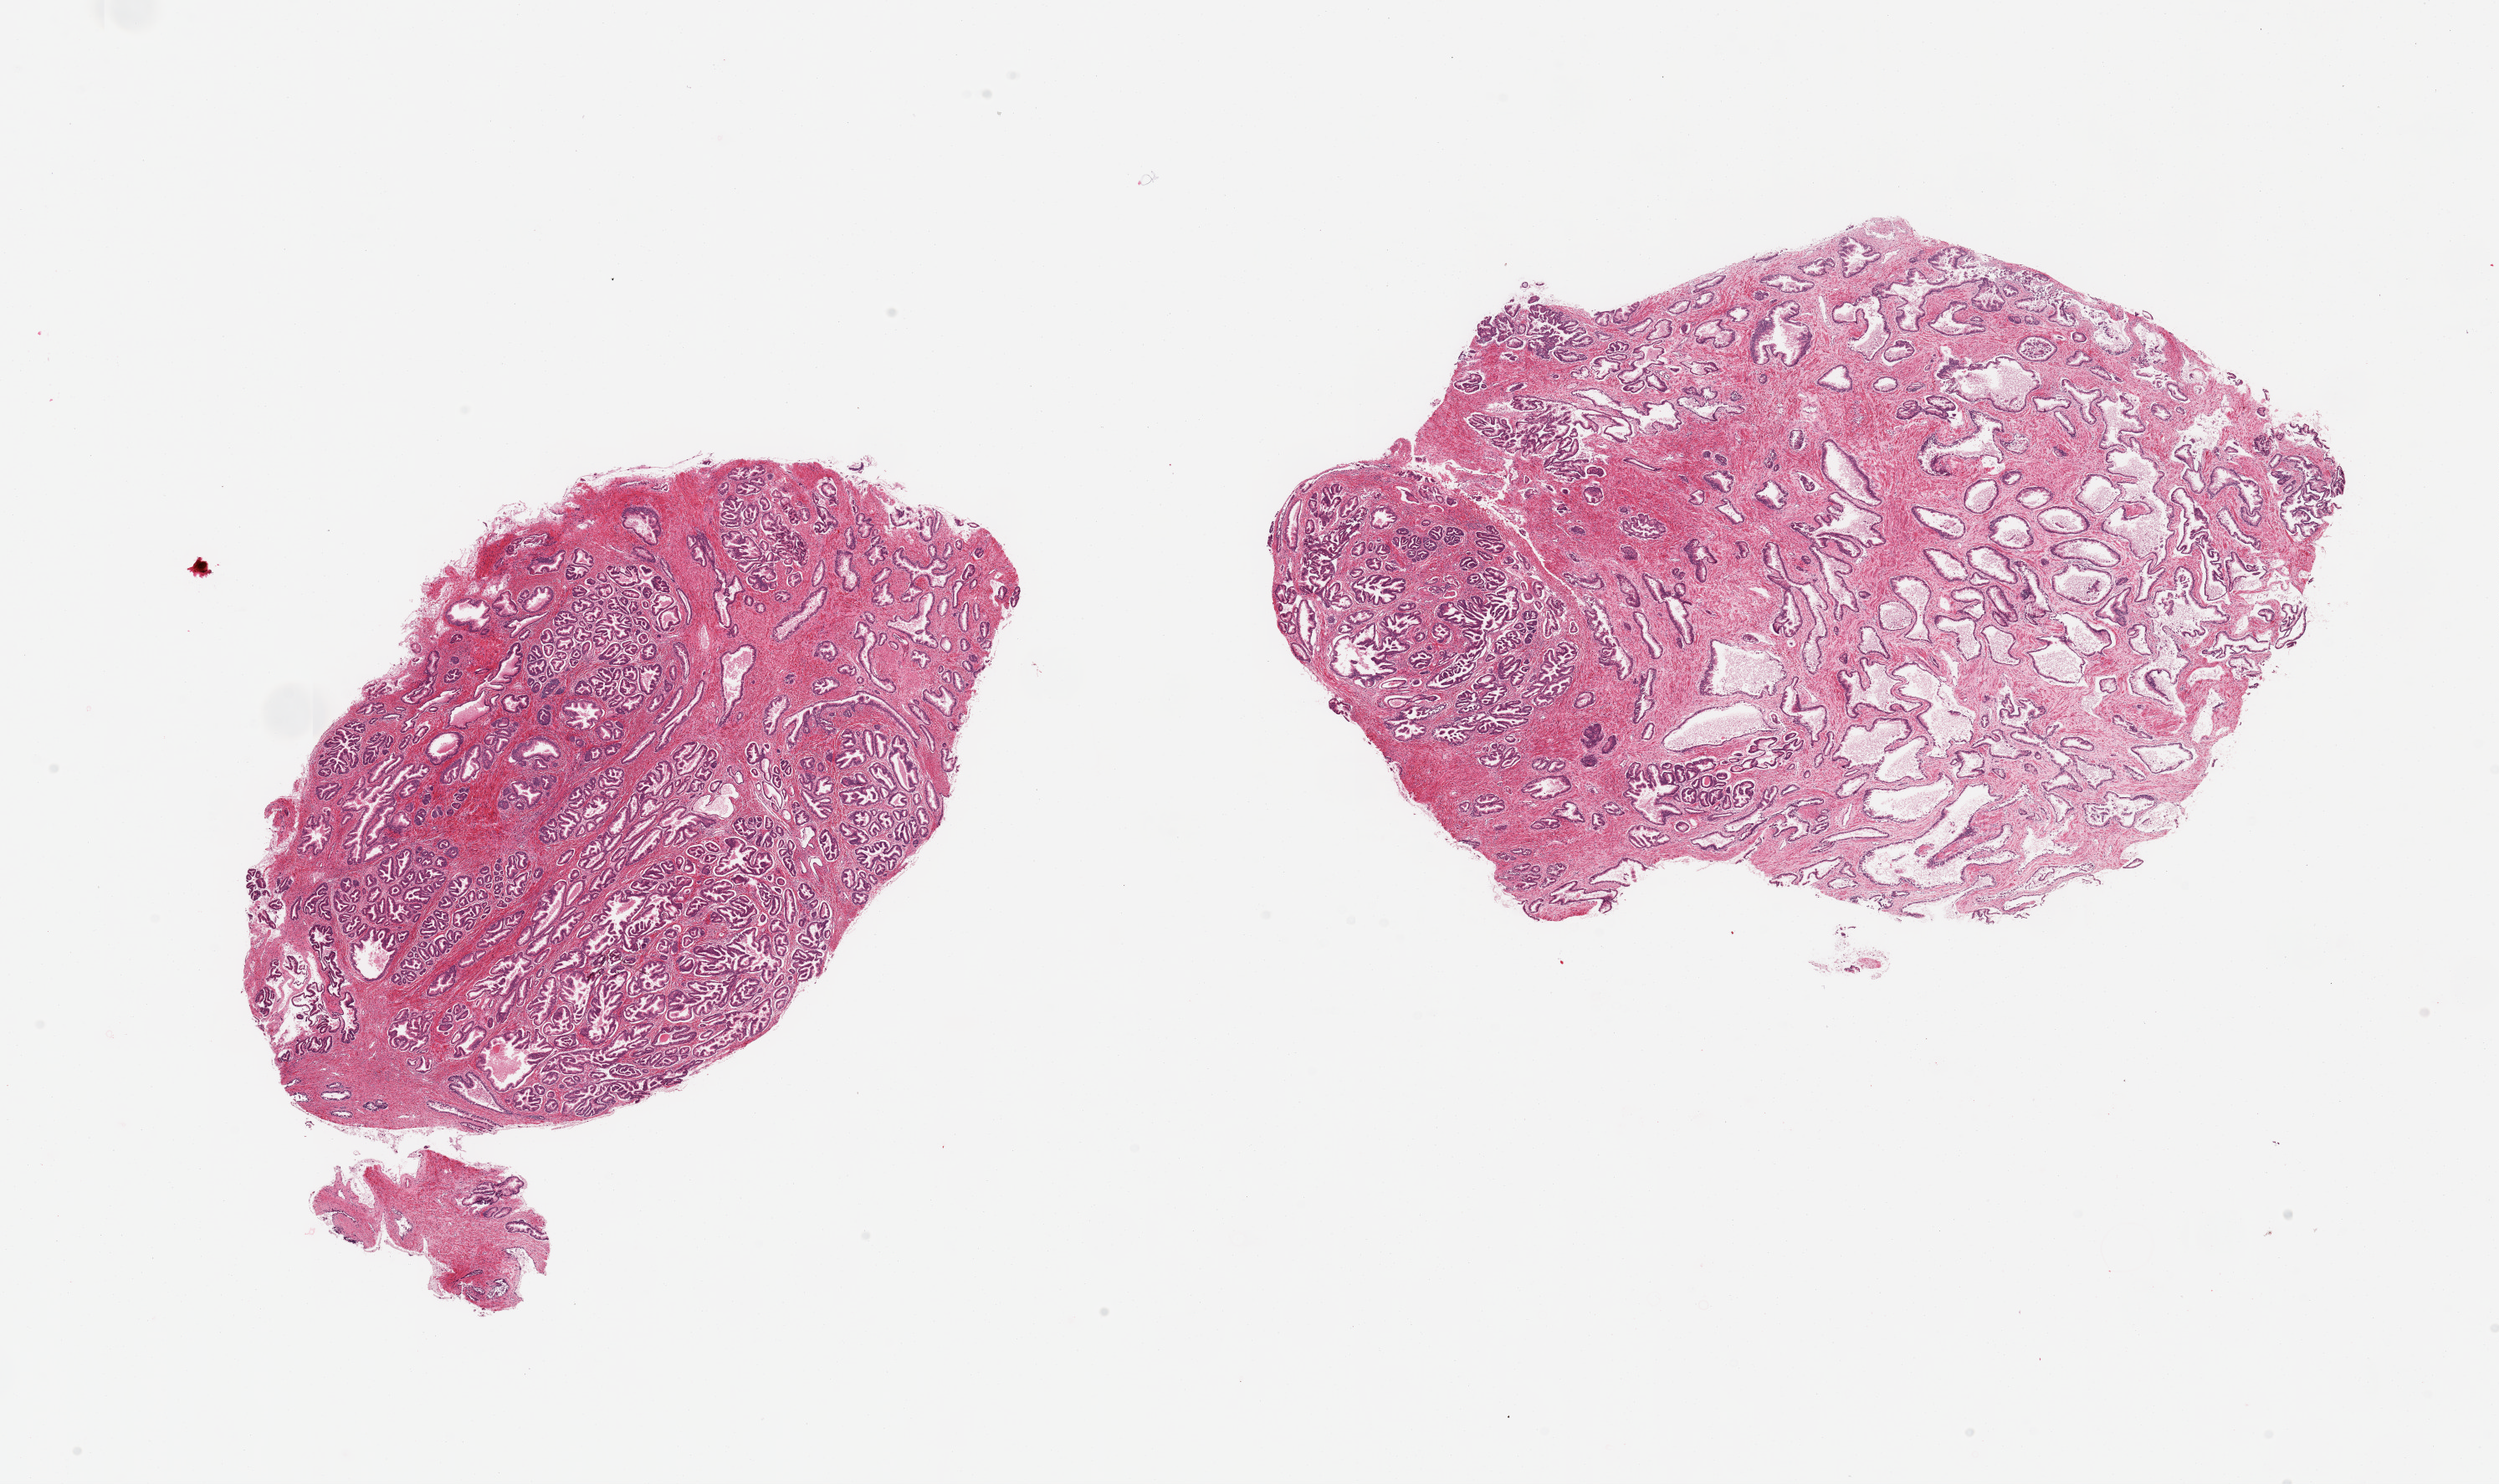
Haematoxylin and eosin whole-slide image — low-resolution overview of the scanned area, about 23.6 x 14.0 mm (acquisition: 20x scan); PAXgene-fixed paraffin-embedded (PFPE) section; sampled site (target tissue): prostate; tissue donor sample.
Pathologist's review note for this sample: 2 pieces, galndular hyperplasia.